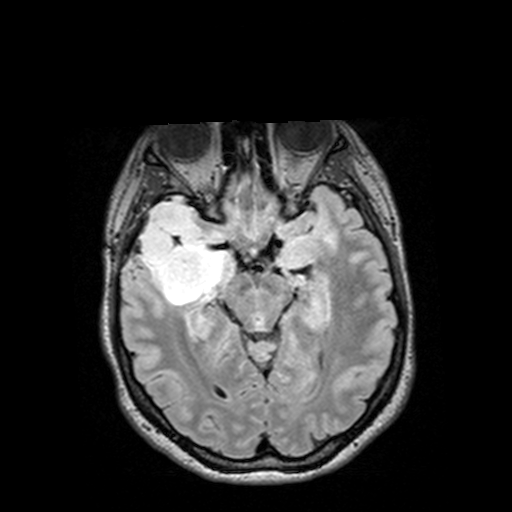
Brain MRI from a brain-tumour surgery series, one axial slice. Slice 85 of 144 in the series (ordered by position). T2 FLAIR. 1 mm slice thickness. 512 × 512 image matrix, field of view 250 × 250 mm. Case-level facts recorded for this patient, not image findings: histopathology: Astrocytoma; WHO grade: 3; IDH mutation: yes.
Annotated regions visible in this slice (expert manual segmentation):
- tumour: bounding box (x1, y1, x2, y2) in pixels: (126, 197, 232, 305)